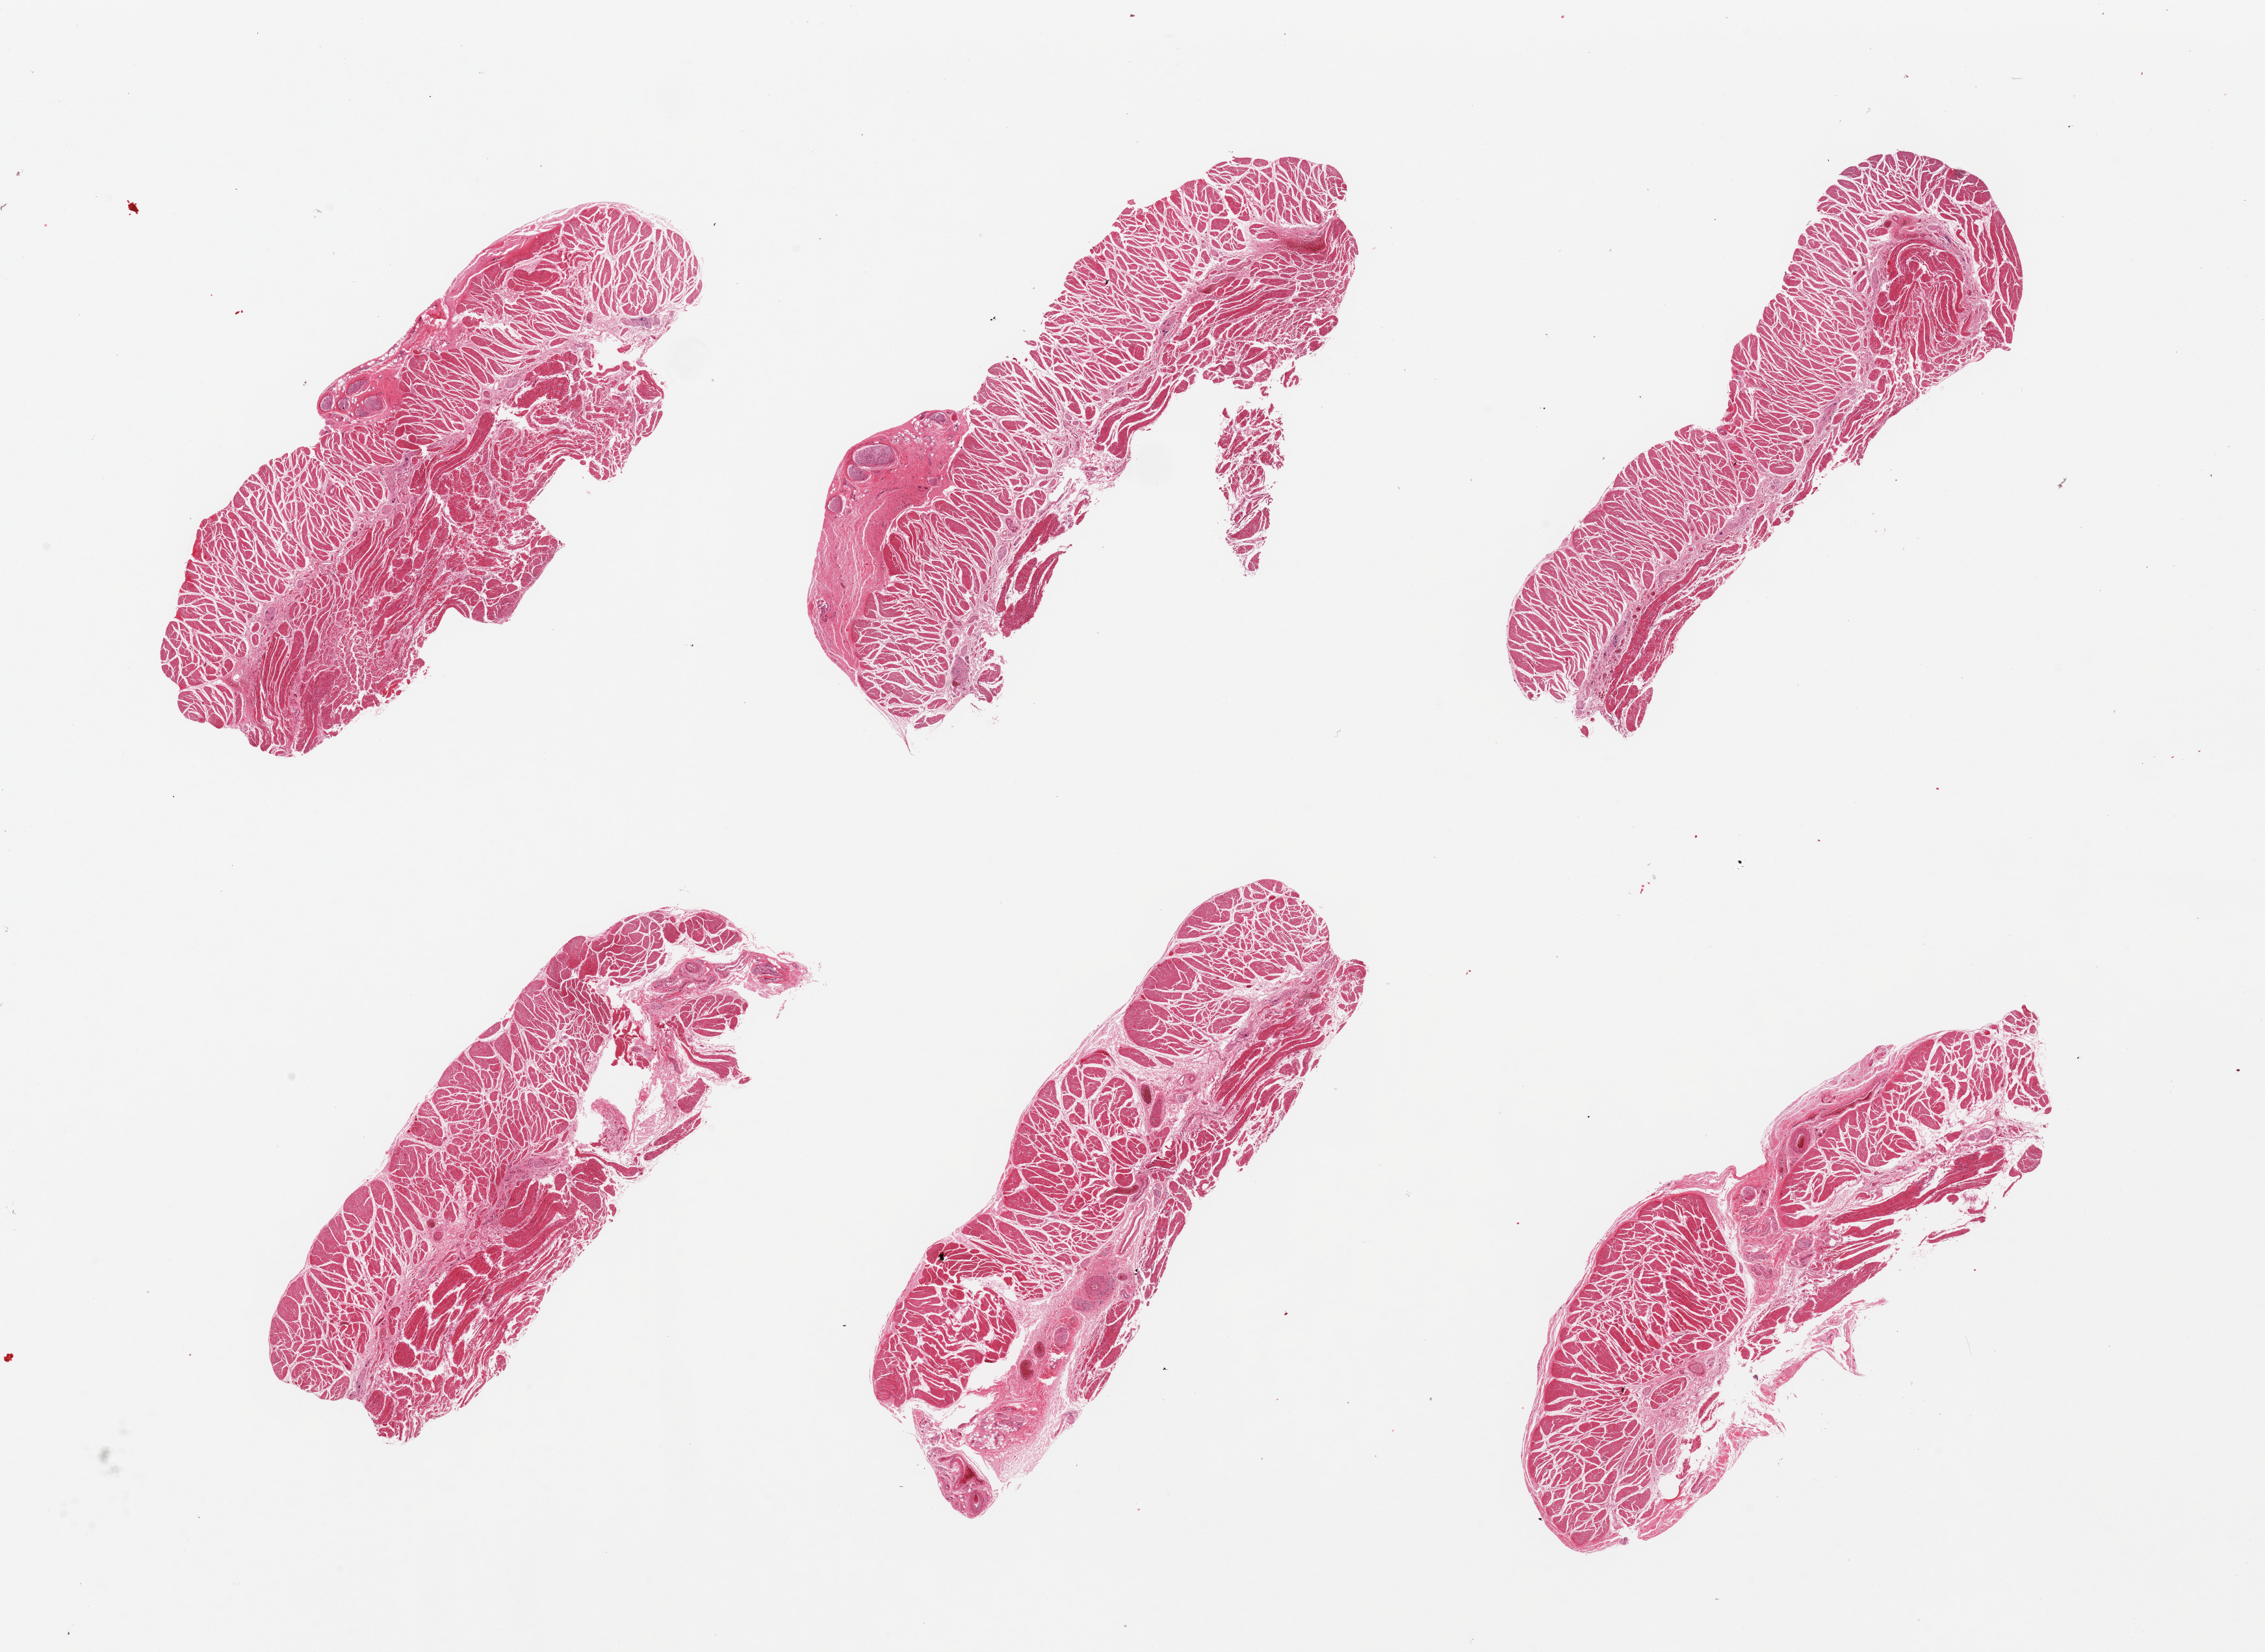
Digitized haematoxylin and eosin-stained section — low-resolution overview of the scanned area, about 27.6 x 20.1 mm (acquisition: 20x scan). PAXgene-fixed, paraffin-embedded tissue. Section of esophageal muscle (target tissue). Tissue donor sample.
• pathologist's review note for this sample: 6 pieces; focal fibrovascular tissue and nerves (less than 10%)